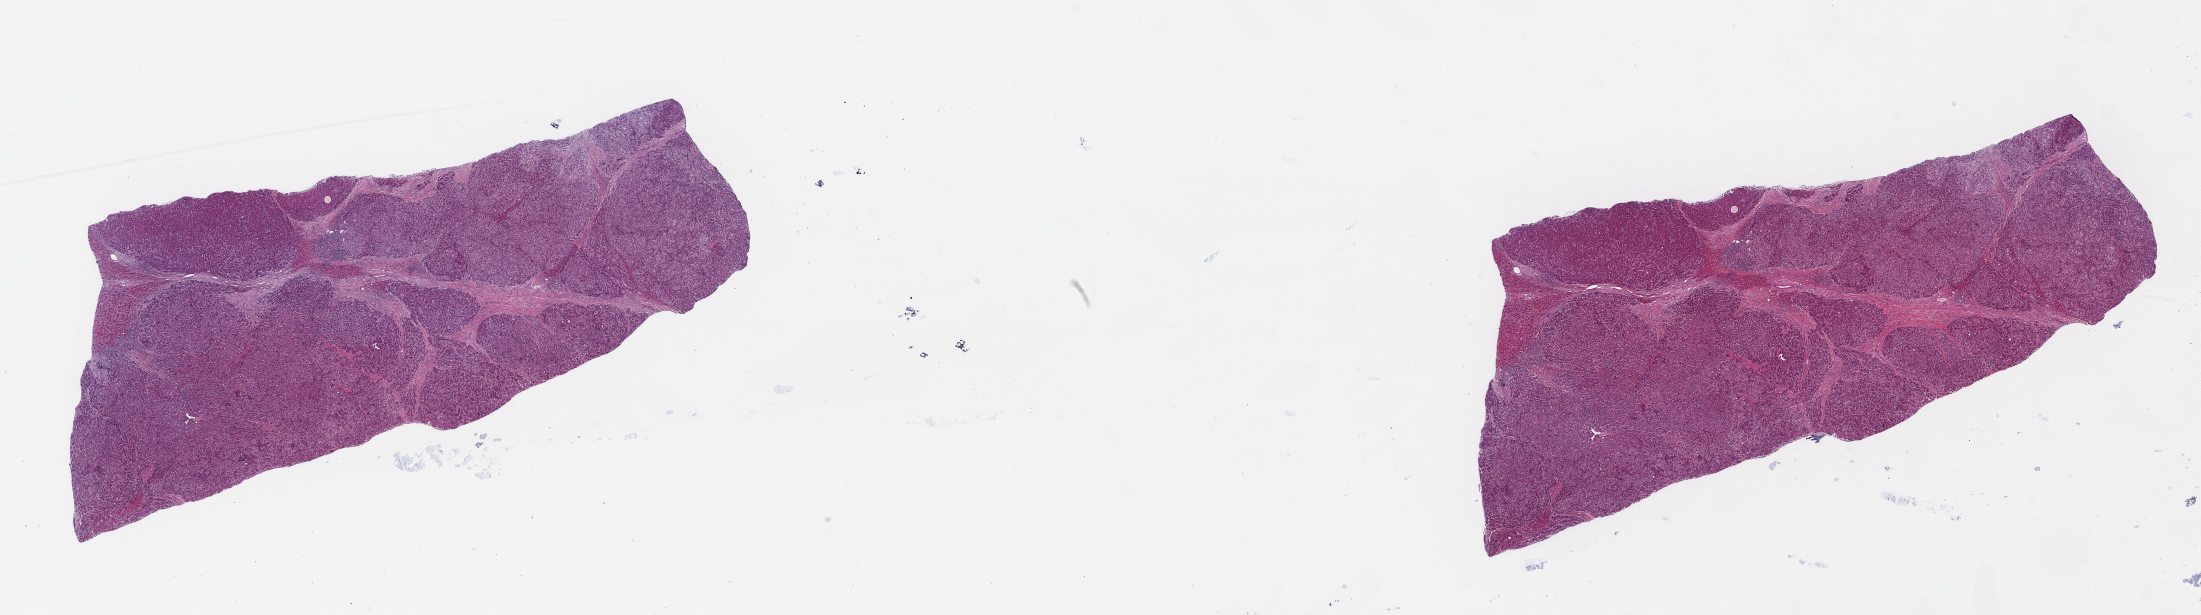
H&E whole-slide image, low-resolution overview of the scanned area, about 34.6 x 9.7 mm, formalin-fixed paraffin-embedded (FFPE) diagnostic section, sample: primary tumour, liver. Male, age 76 years at initial diagnosis.
Pathologic diagnosis: Hepatocellular carcinoma, NOS.